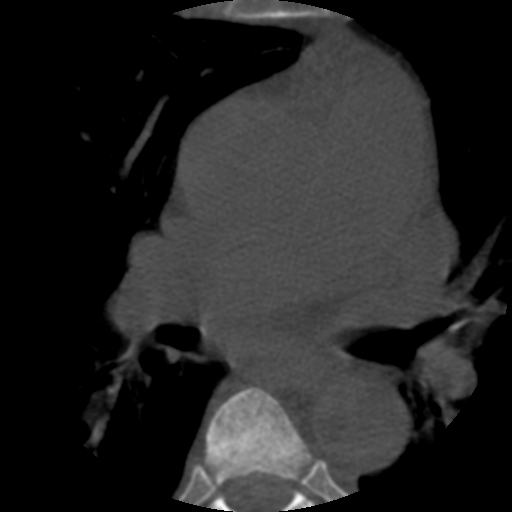
CT including the spine, one axial slice. Slice 366 of 508 in the series (ordered by position). Reconstruction kernel STANDARD. 120 kVp. Bone window (W 1800 / L 400 HU). 512 × 512 image matrix, field of view 160 × 160 mm. Patient age 57 years. Case-level facts recorded for this patient, not image findings: primary cancer: prostate.
Structures marked on this image (semi-automatically segmented with operator editing):
- T5 vertebra: bounding box <206,387,309,489> (left, top, right, bottom; pixels)
- T6 vertebra: <211,476,312,512>